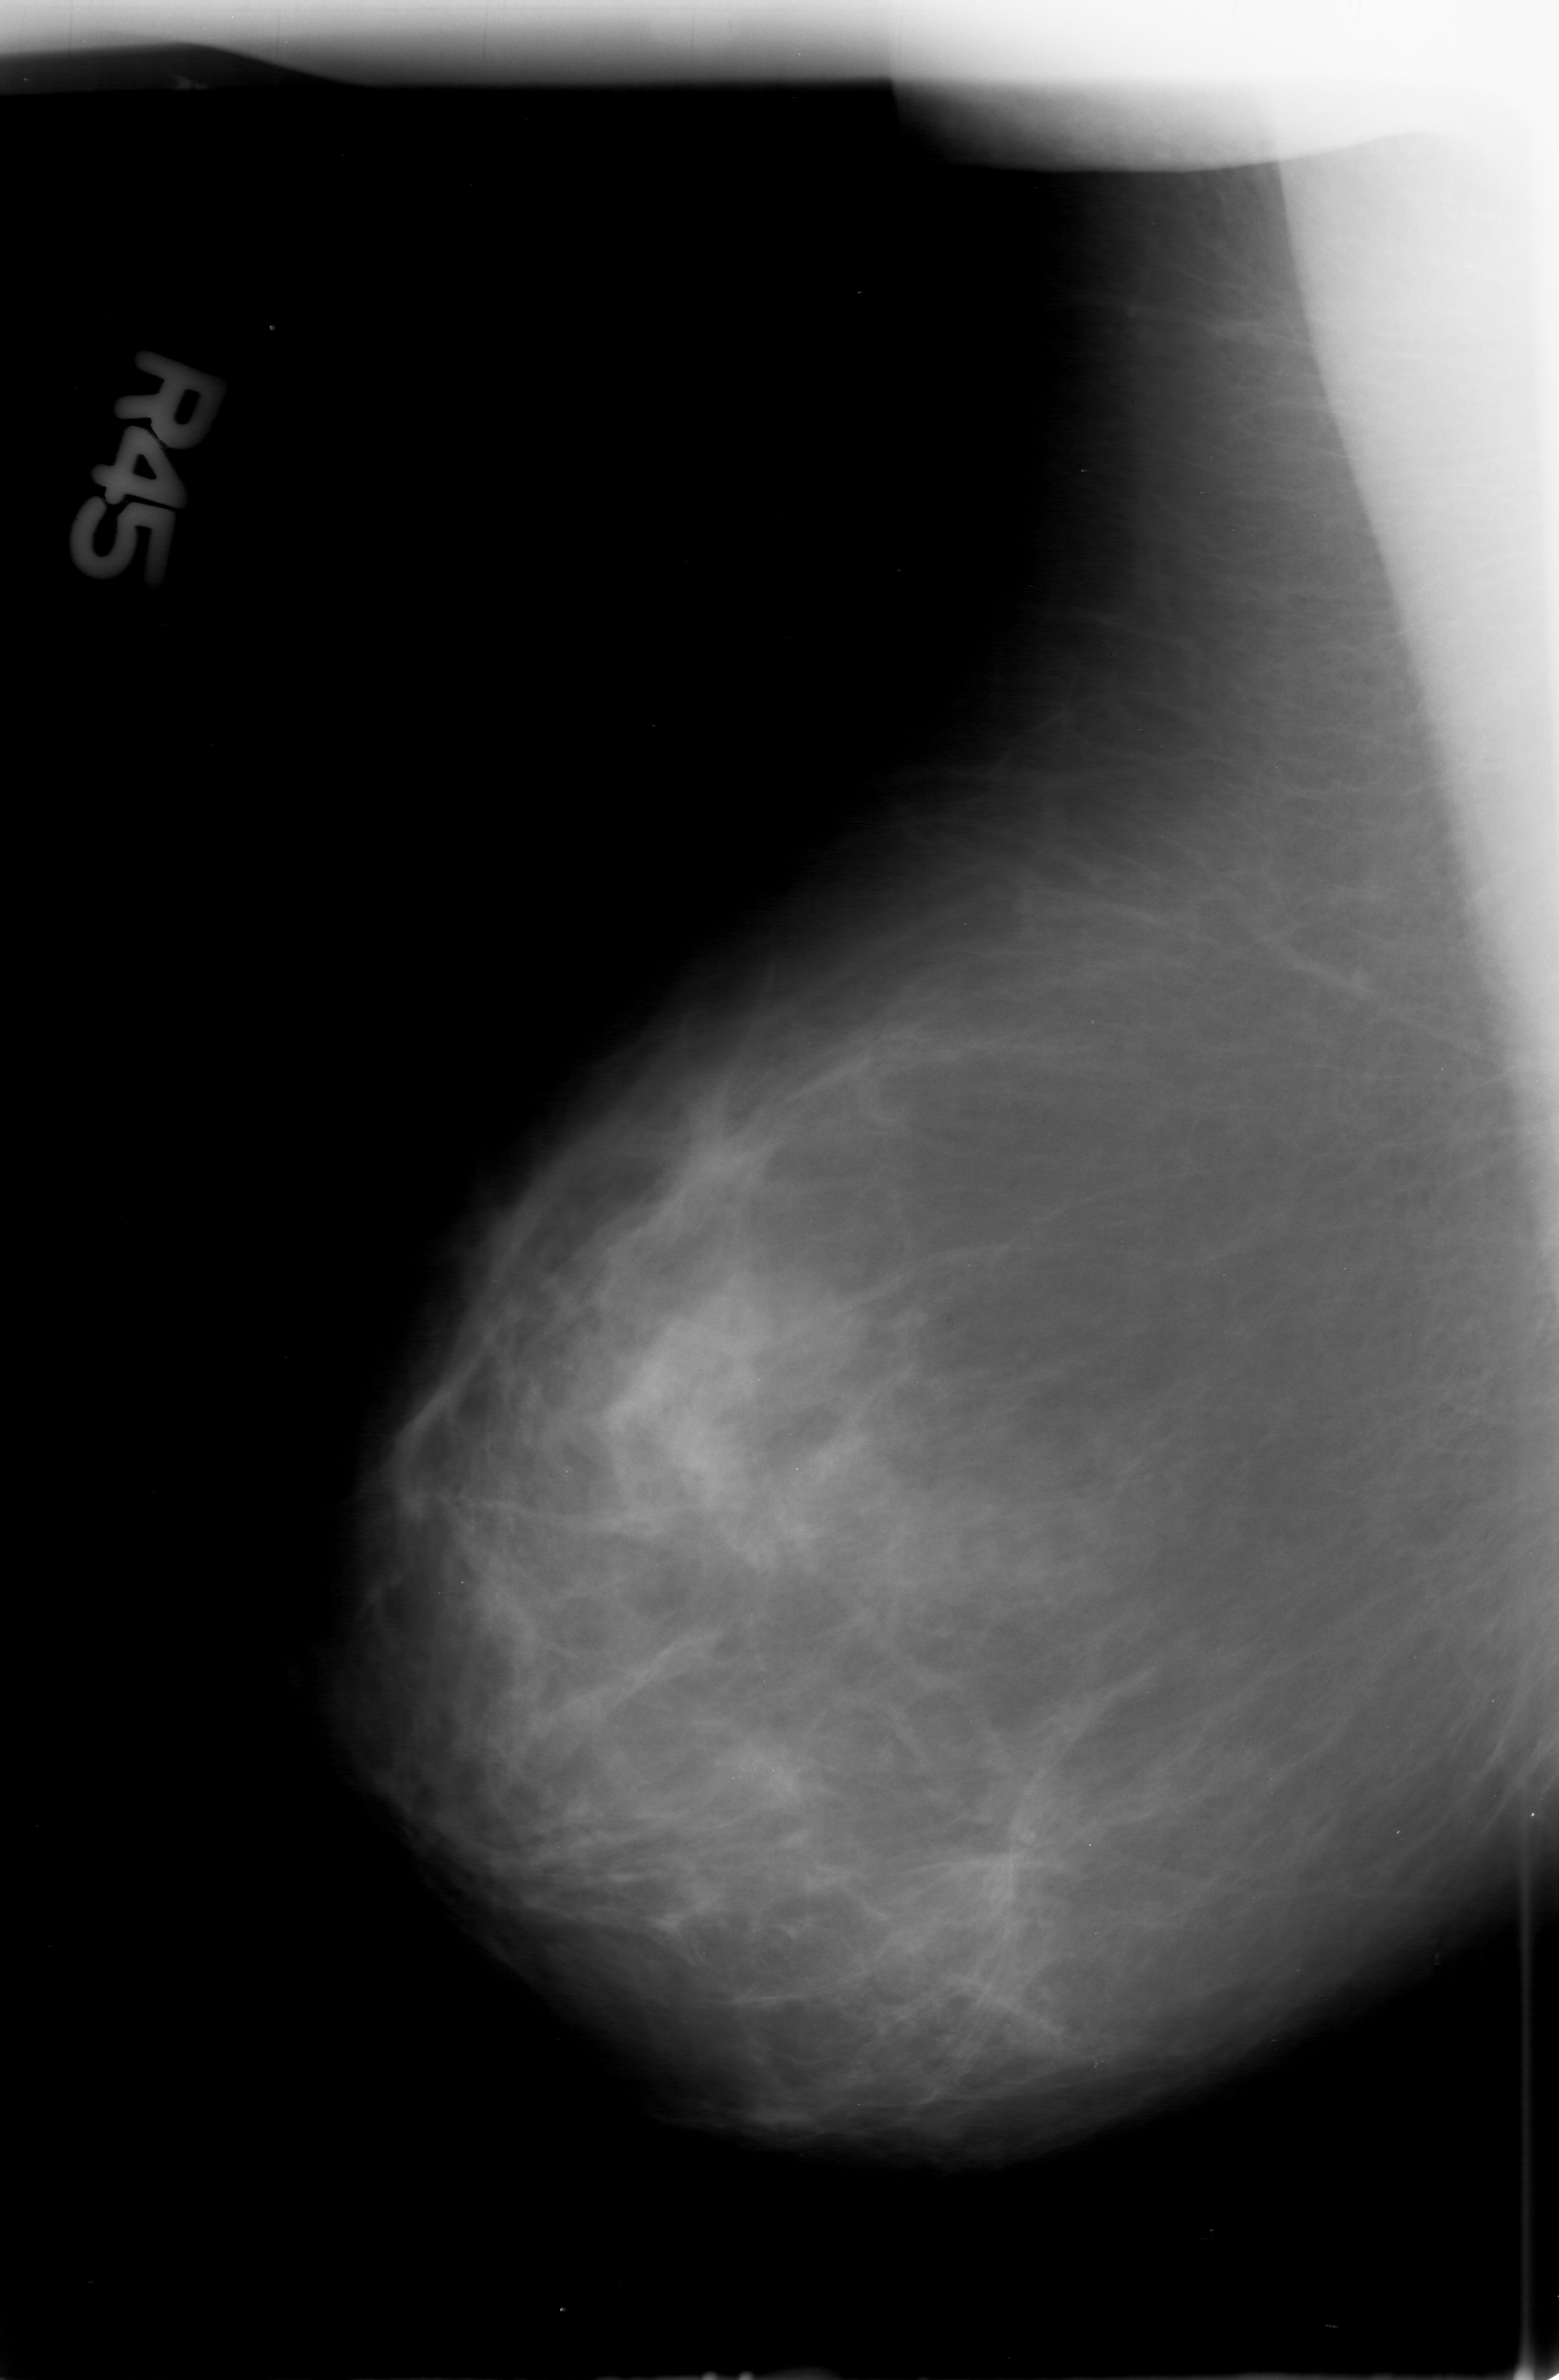
Mammogram (digitized film), right breast, mediolateral oblique (MLO) view, breast composition: scattered fibroglandular densities (BI-RADS density category 2 of 4).
- Calcifications, morphology pleomorphic, distribution clustered; BI-RADS assessment category 0; pathology (as recorded): malignant.